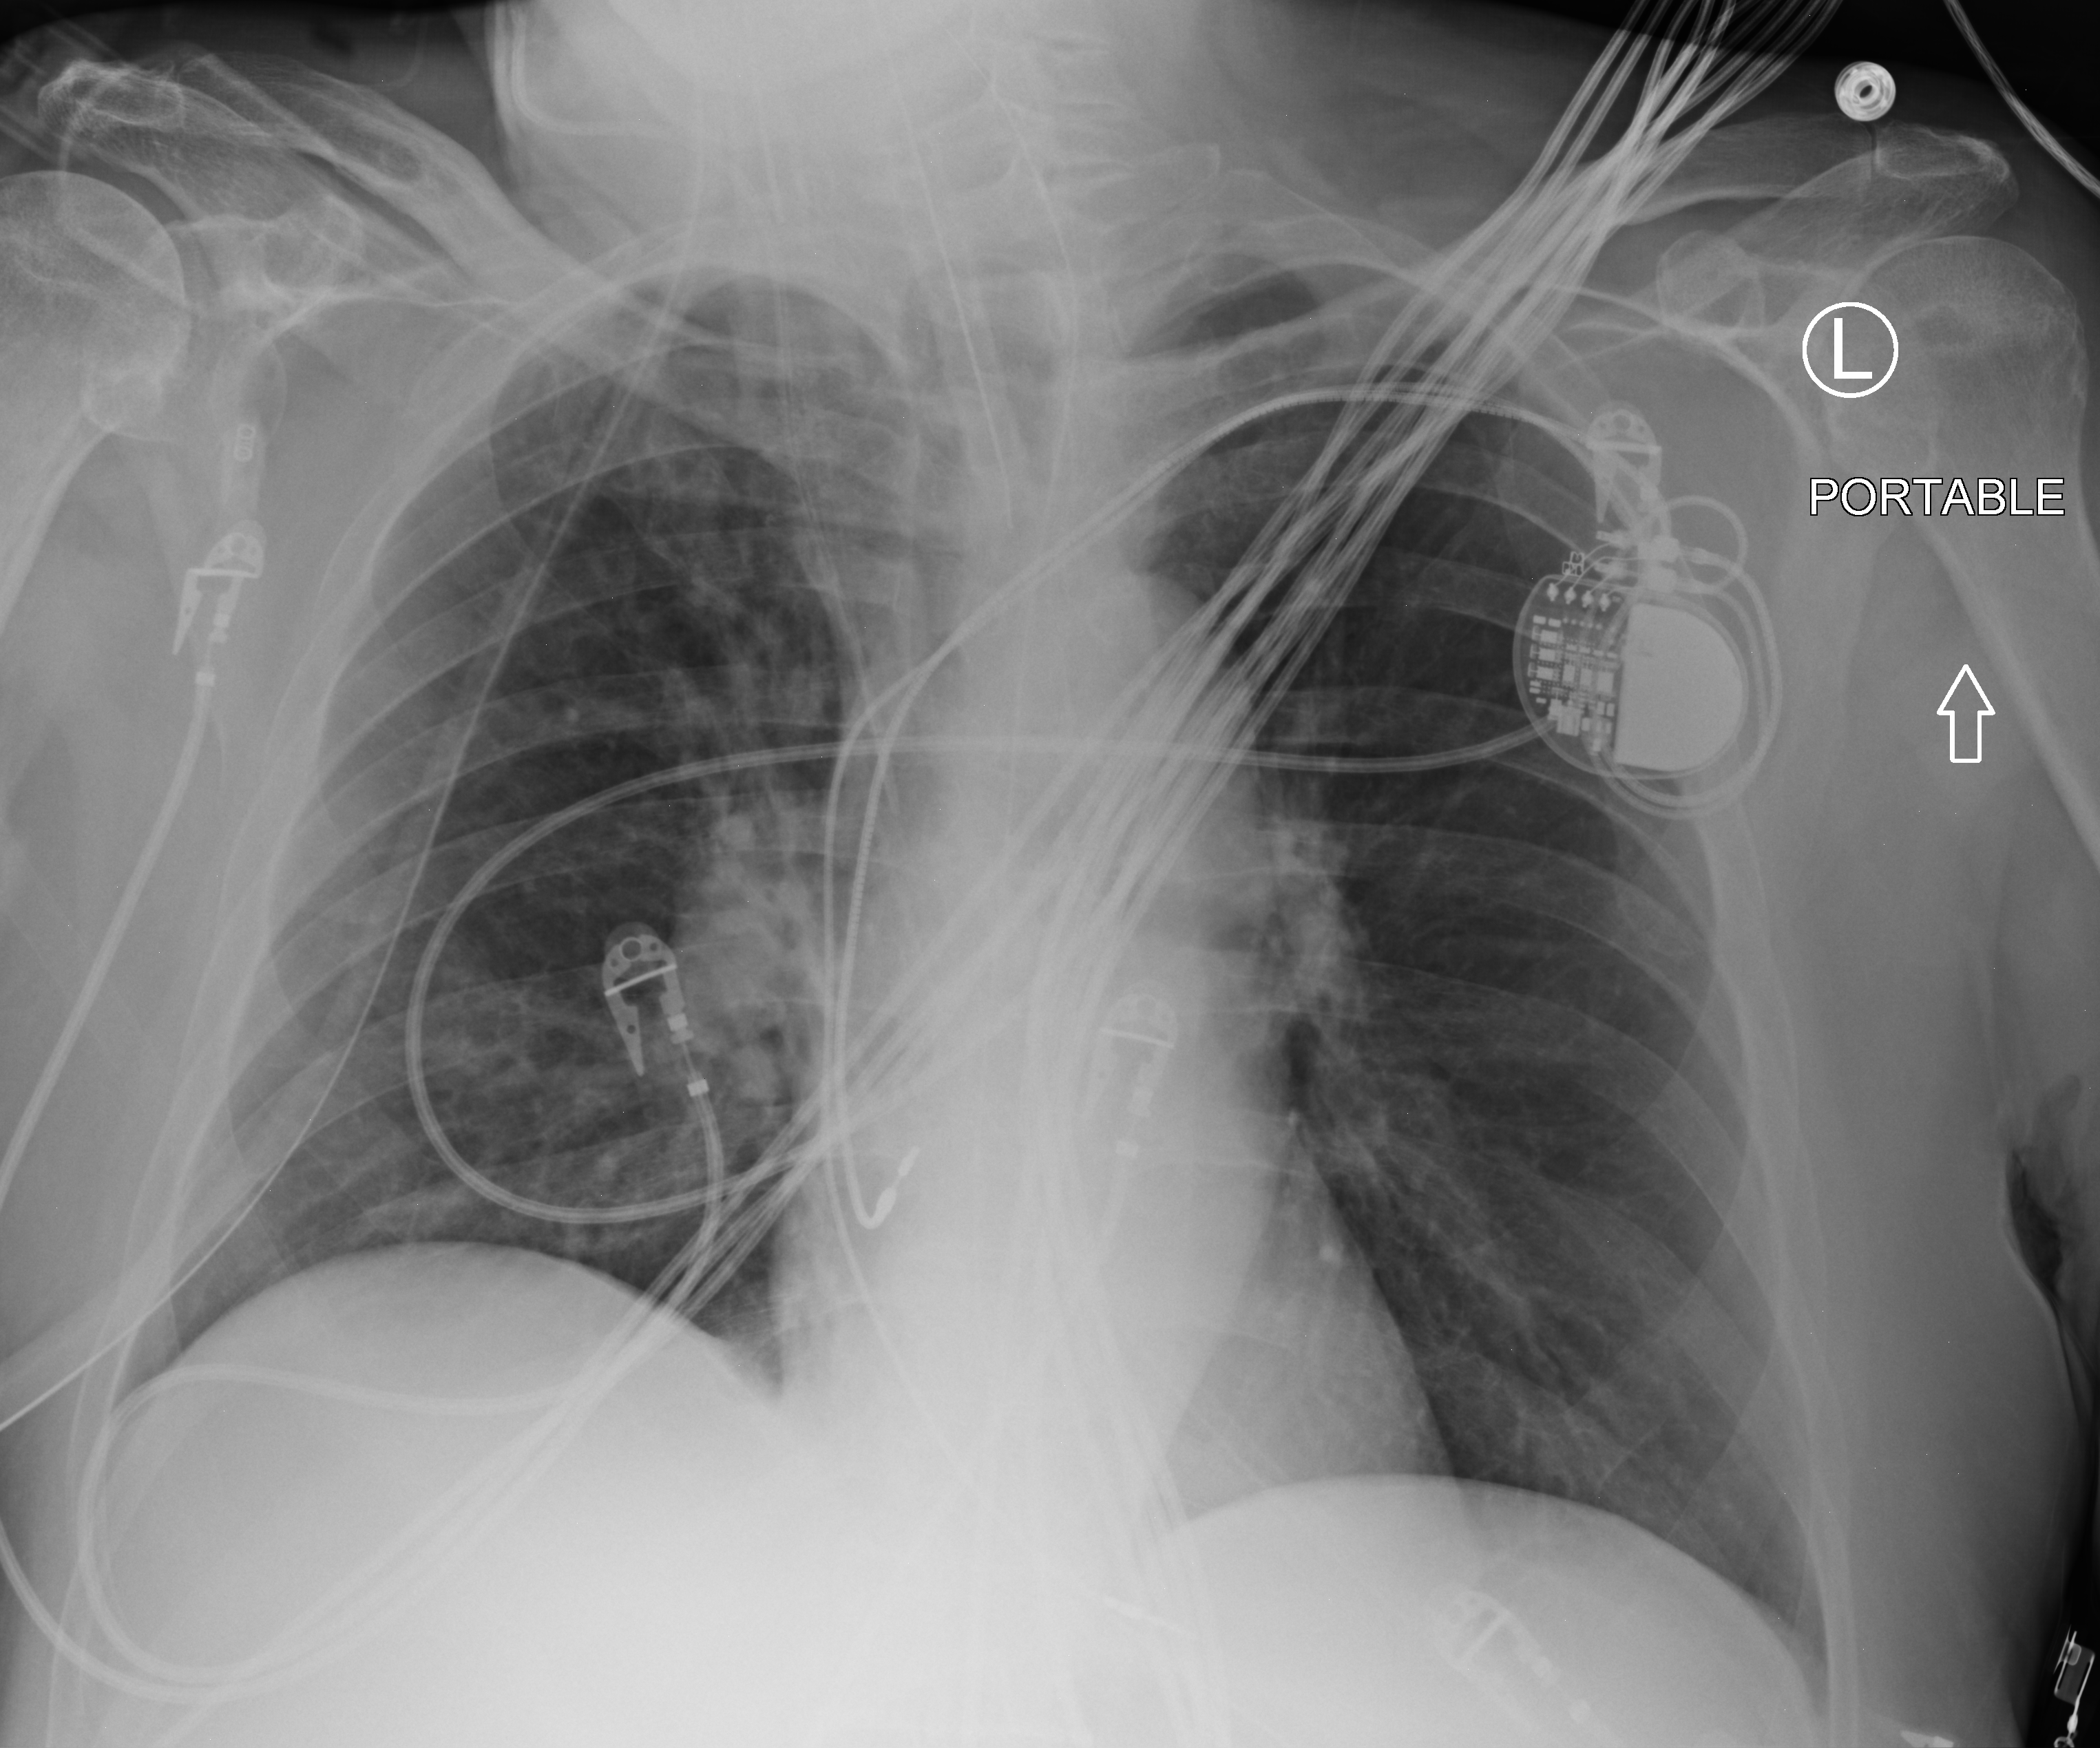
Portable chest radiograph; anteroposterior (AP) projection. Male patient hospitalised with COVID-19, age 60–74 years.
From the hospital-stay record, not from the radiograph (when in the stay this image was taken is not recorded): admitted to intensive care during this hospital stay: no; COPD (admission record): yes; length of hospital stay: 6 days.